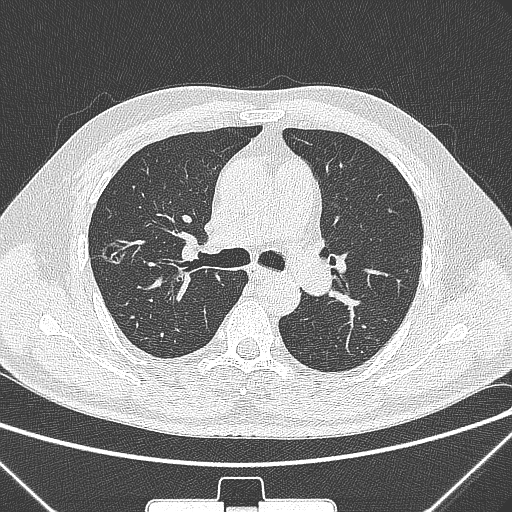
Chest CT, one axial slice. Slice 195 of 320 in the series (ordered by position). 120 kVp. Lung window (W 1500 / L -600 HU). 1 mm slice thickness. 512 × 512 image matrix, field of view 350 × 350 mm. Male patient, age 58 years. From the clinical record (not read from this slice): clinical TNM (as recorded): T1c N0 M0.
Annotated regions visible in this slice (rectangle marked by the reading radiologist):
- lung tumour (recorded histology: adenocarcinoma): bounding box [x1, y1, x2, y2] px = [90, 239, 136, 273]